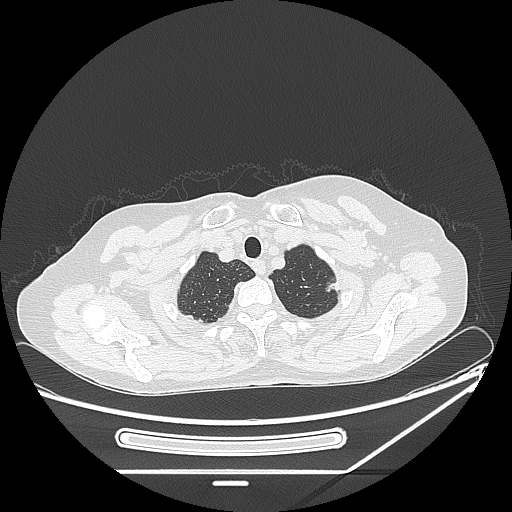
Chest CT, one axial slice. Position 216 of 250 along the scan axis. Reconstruction kernel LUNG. 120 kVp. Lung window (W 1500 / L -600 HU). 1.25 mm slice thickness. 512 × 512 image matrix, field of view 409 × 409 mm. Patient: female, 57 years. Case-level facts recorded for this patient, not image findings: clinical TNM (as recorded): T1c N0 M0; histopathological grade: G2-3.
Annotated regions visible in this slice (rectangle marked by the reading radiologist):
- lung tumour (recorded histology: adenocarcinoma): box from (x=324, y=275) to (x=341, y=300) px